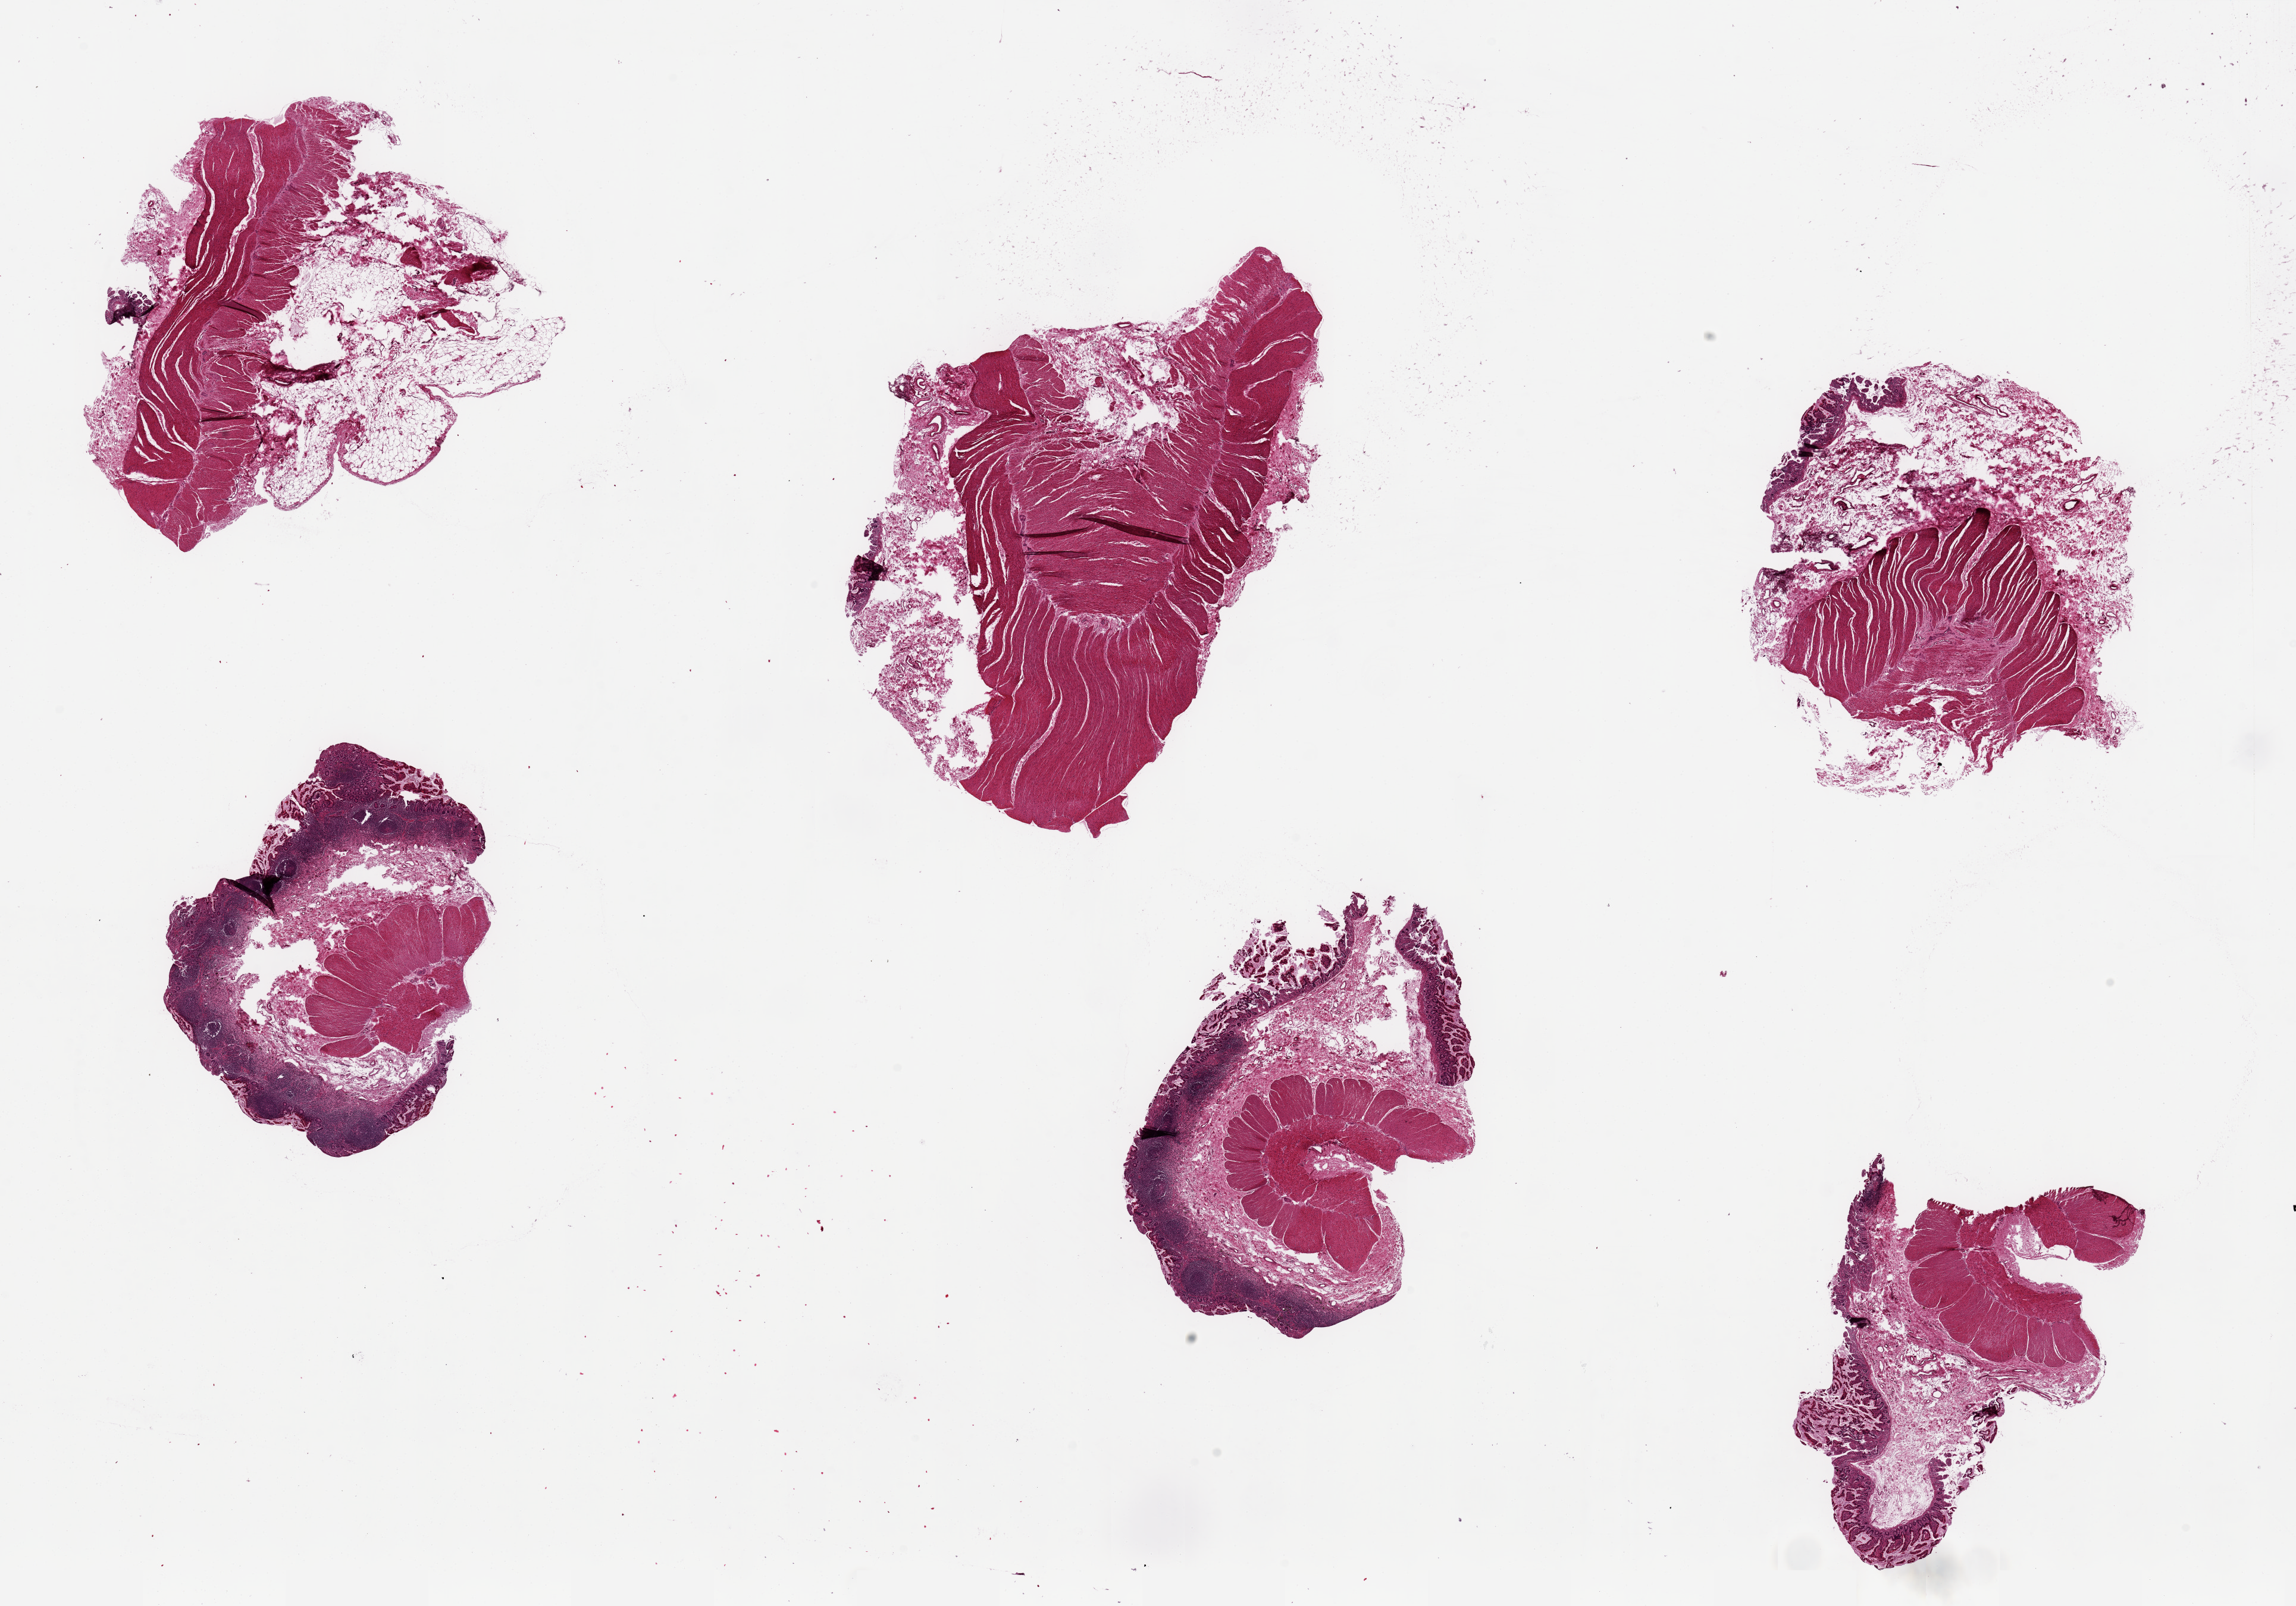
Whole-slide image, H&E stain, brightfield, a low-resolution overview of the entire scanned area, about 30.5 x 21.4 mm (from a 20x scan), PAXgene-fixed paraffin-embedded (PFPE) section, target tissue: ileum, donor tissue sample. Male donor.
Reviewer comment on this tissue sample: 6 pieces ~6x5mm, 2 with abundant lymphoid elements, rest with tract, largely muscle and/or mucosa.